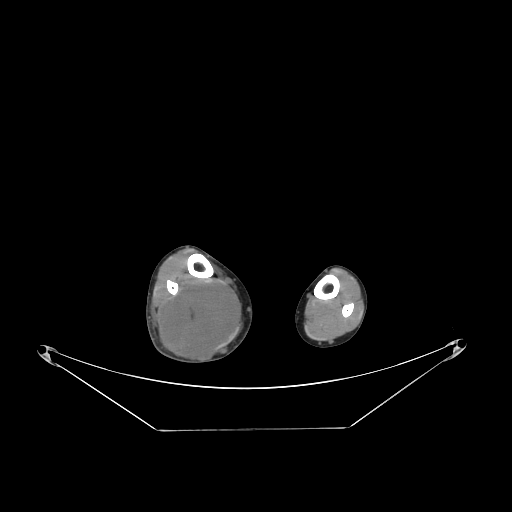
CT of an extremity soft-tissue mass (from a PET/CT study), one axial slice; slice 74 of 267 in the series (ordered by position); reconstruction kernel STANDARD; 140 kVp; soft-tissue window (W 400 / L 40 HU); 3.75 mm slice thickness; 512 × 512 image matrix. Male patient. From the clinical record (not read from this slice): histological type: liposarcoma - round cell; grade: high; site of the primary tumour: right calf.
Annotated regions visible in this slice (expert contour drawn on MRI and transferred to this co-registered scan by the dataset authors):
- gross tumour volume (mass): box from (x=158, y=279) to (x=239, y=364) px